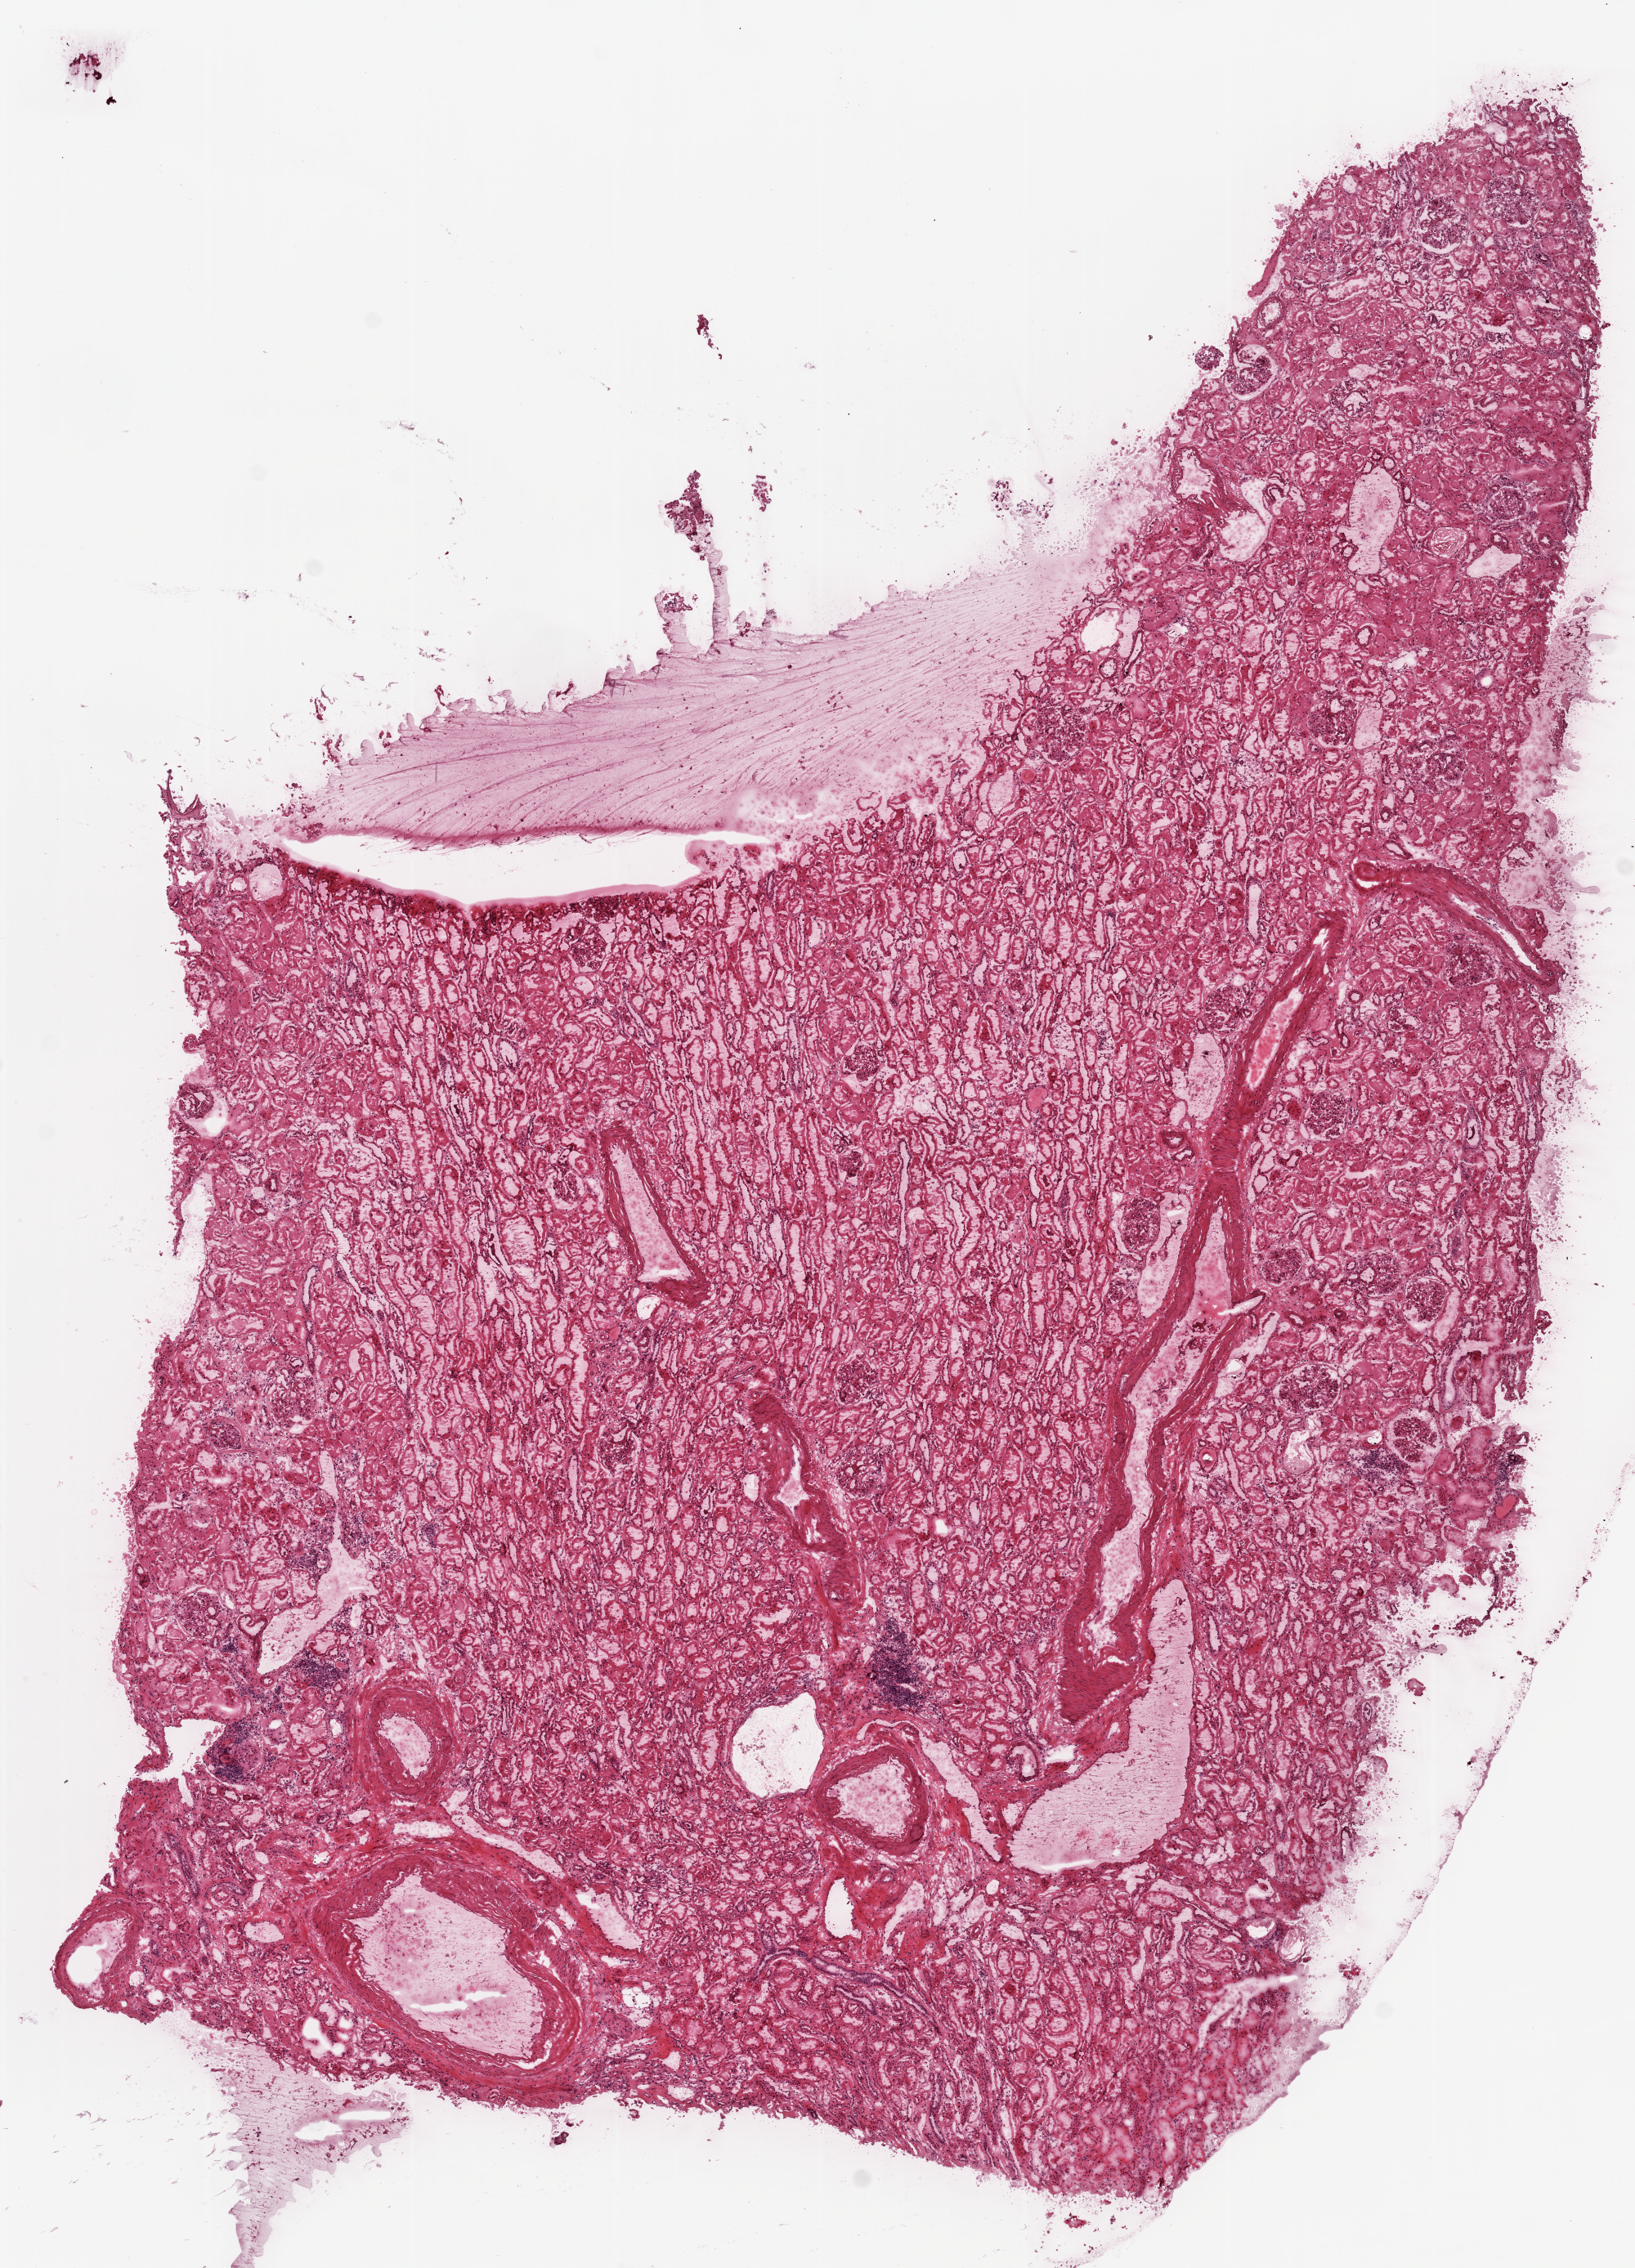
H&E-stained whole-slide image, whole scanned area (about 8.0 x 11.1 mm, from a 20x scan) shown as a low-resolution overview. Frozen section from the top of the tissue portion. Sample: solid tissue normal (non-tumour tissue), kidney. Male, age 70 years at initial diagnosis.
- this section: solid tissue normal (non-tumour) sample from the same patient
- patient diagnosis: Clear cell adenocarcinoma, NOS